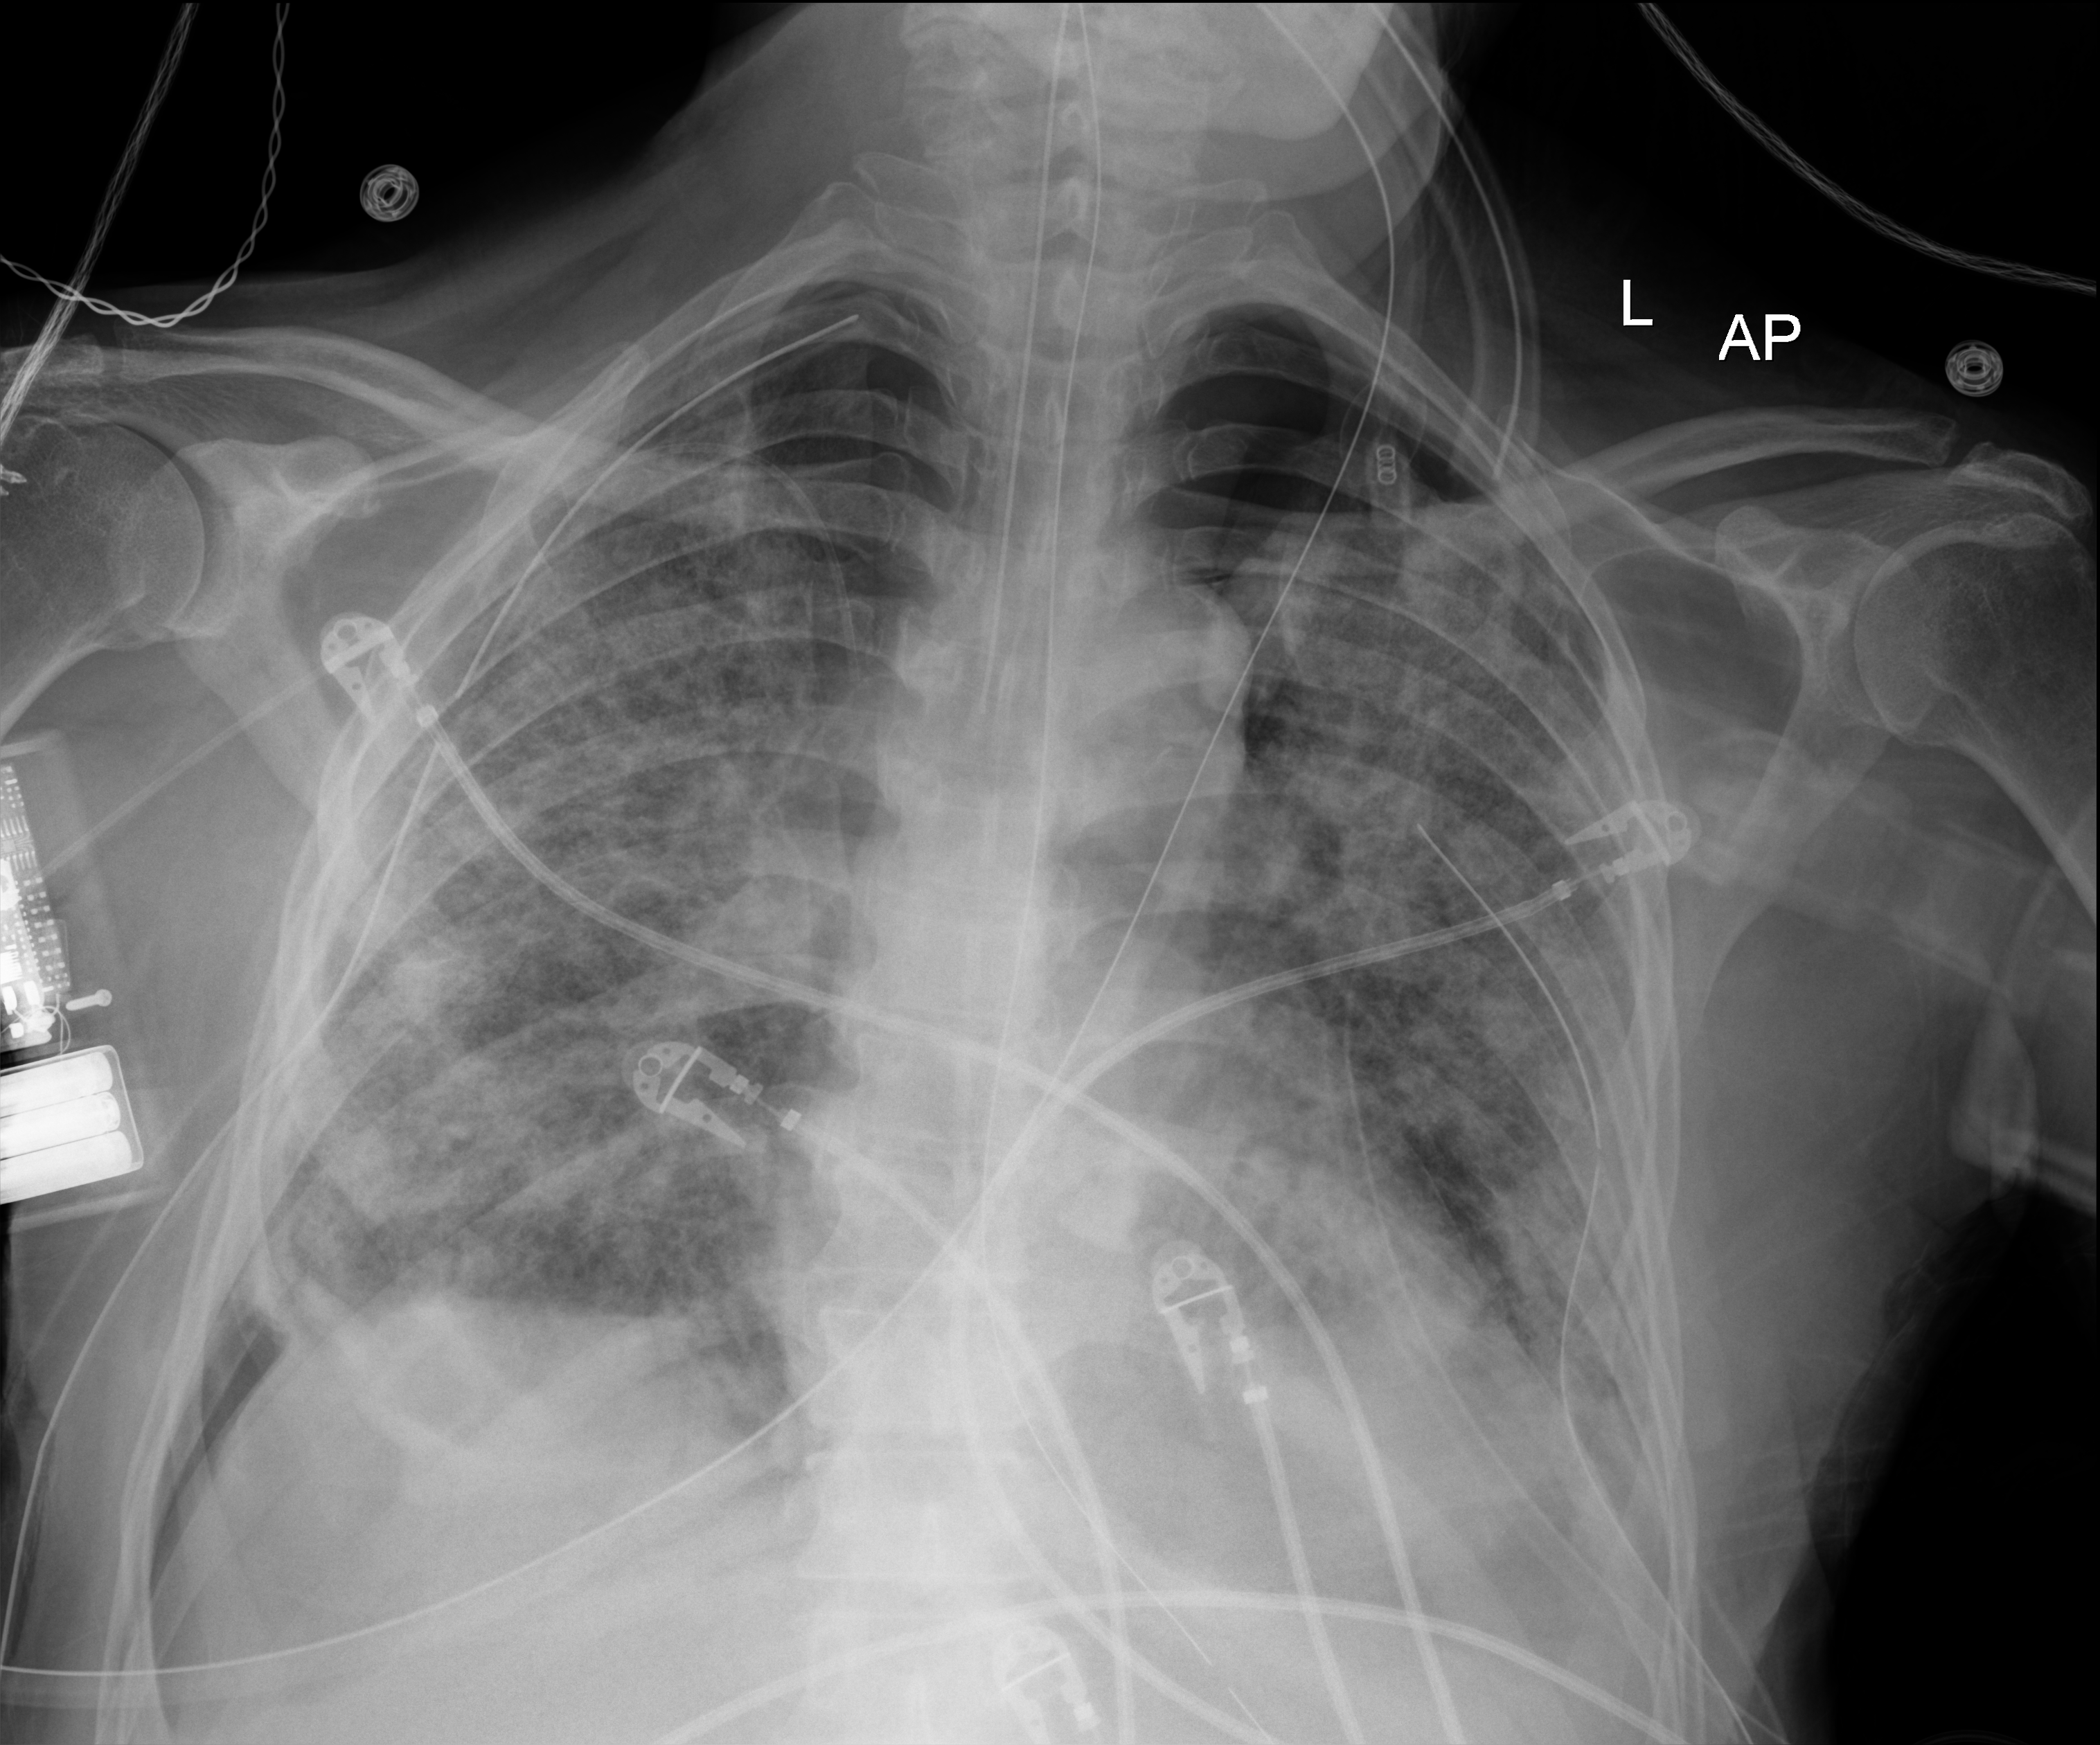
Bedside chest radiograph (digital radiography); anteroposterior (AP) projection. Patient hospitalised with COVID-19; male, aged 60–74 years.
Hospital-stay facts (about this admission, not read from this image; timing relative to this image not recorded): hypertension (admission record): no; admitted to intensive care during this hospital stay: yes.